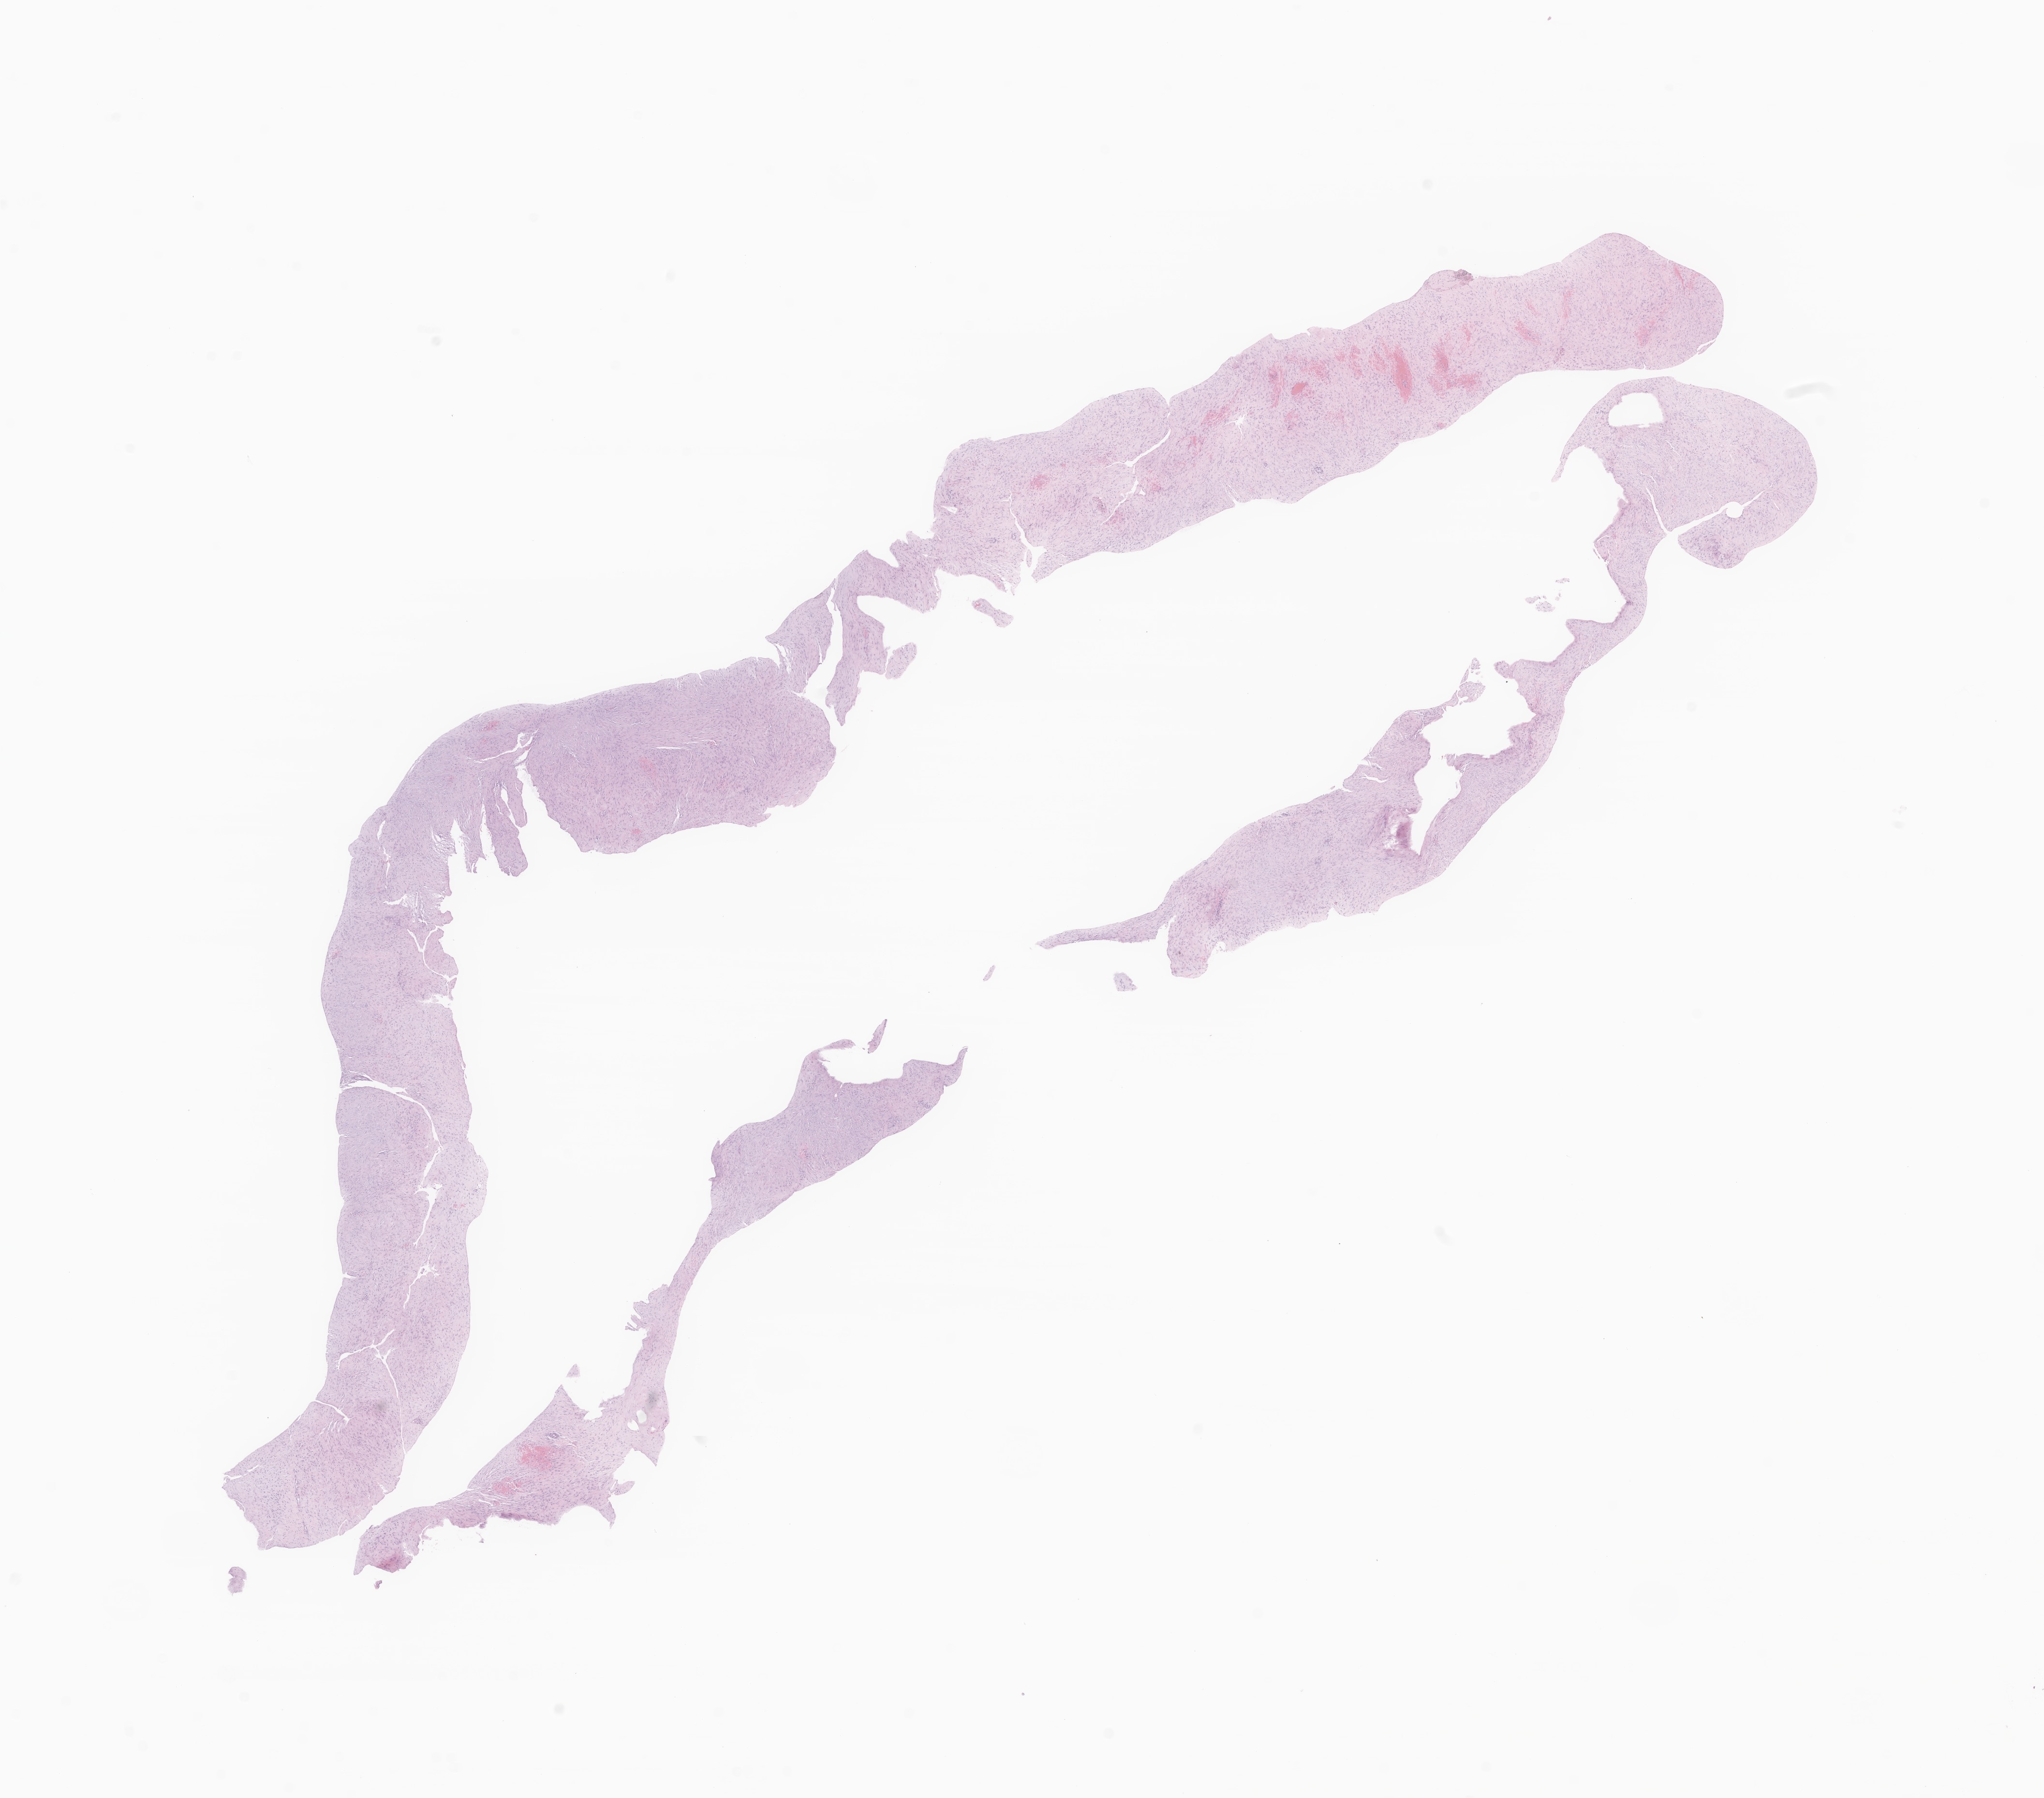
H&E whole-slide image of tumor tissue from the peritoneum, low-resolution overview of the scanned area, about 17.8 x 15.7 mm; formalin-fixed paraffin-embedded section. Patient male; age 212 months (17 years 8 months).
Diagnosis (ICD-O-3 morphology term): Aggressive fibromatosis.